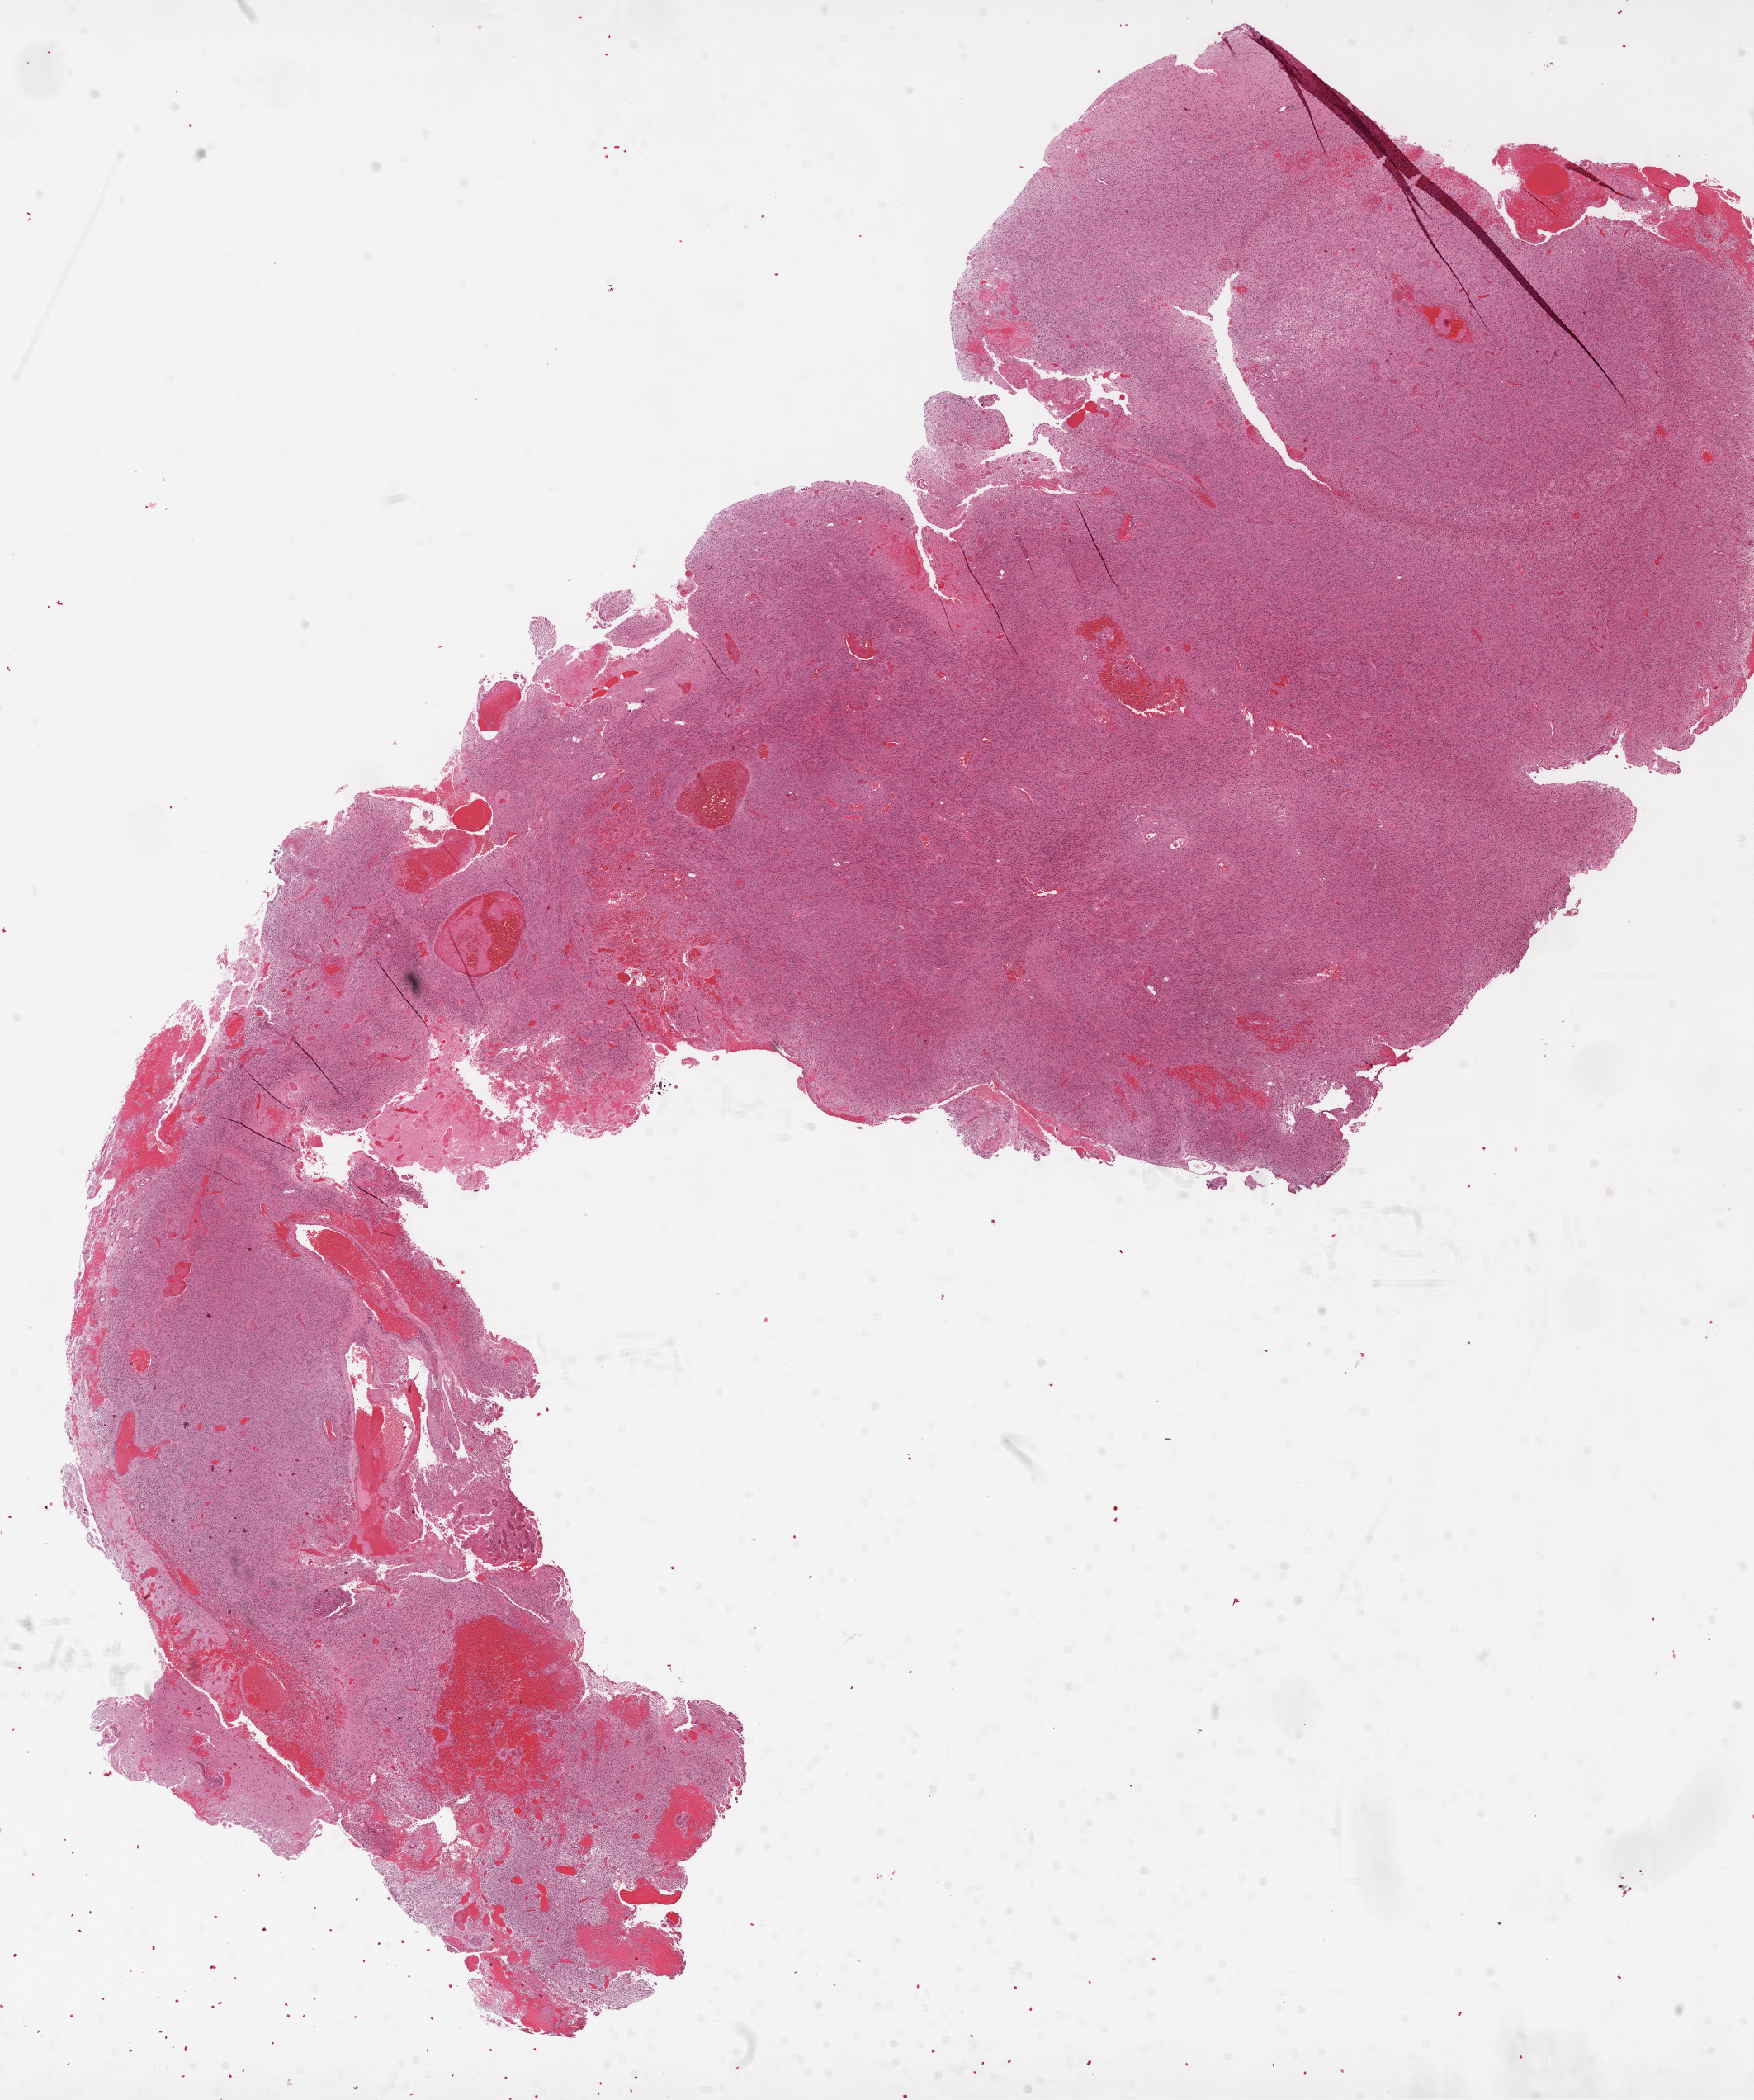
Hematoxylin and eosin (H&E) stained whole-slide image, low-resolution overview of the scanned area, about 17.1 x 20.4 mm. Formalin-fixed paraffin-embedded (FFPE) diagnostic section. Sample: primary tumour, brain. Female patient; age at initial diagnosis 58 years.
- pathologic diagnosis: Glioblastoma